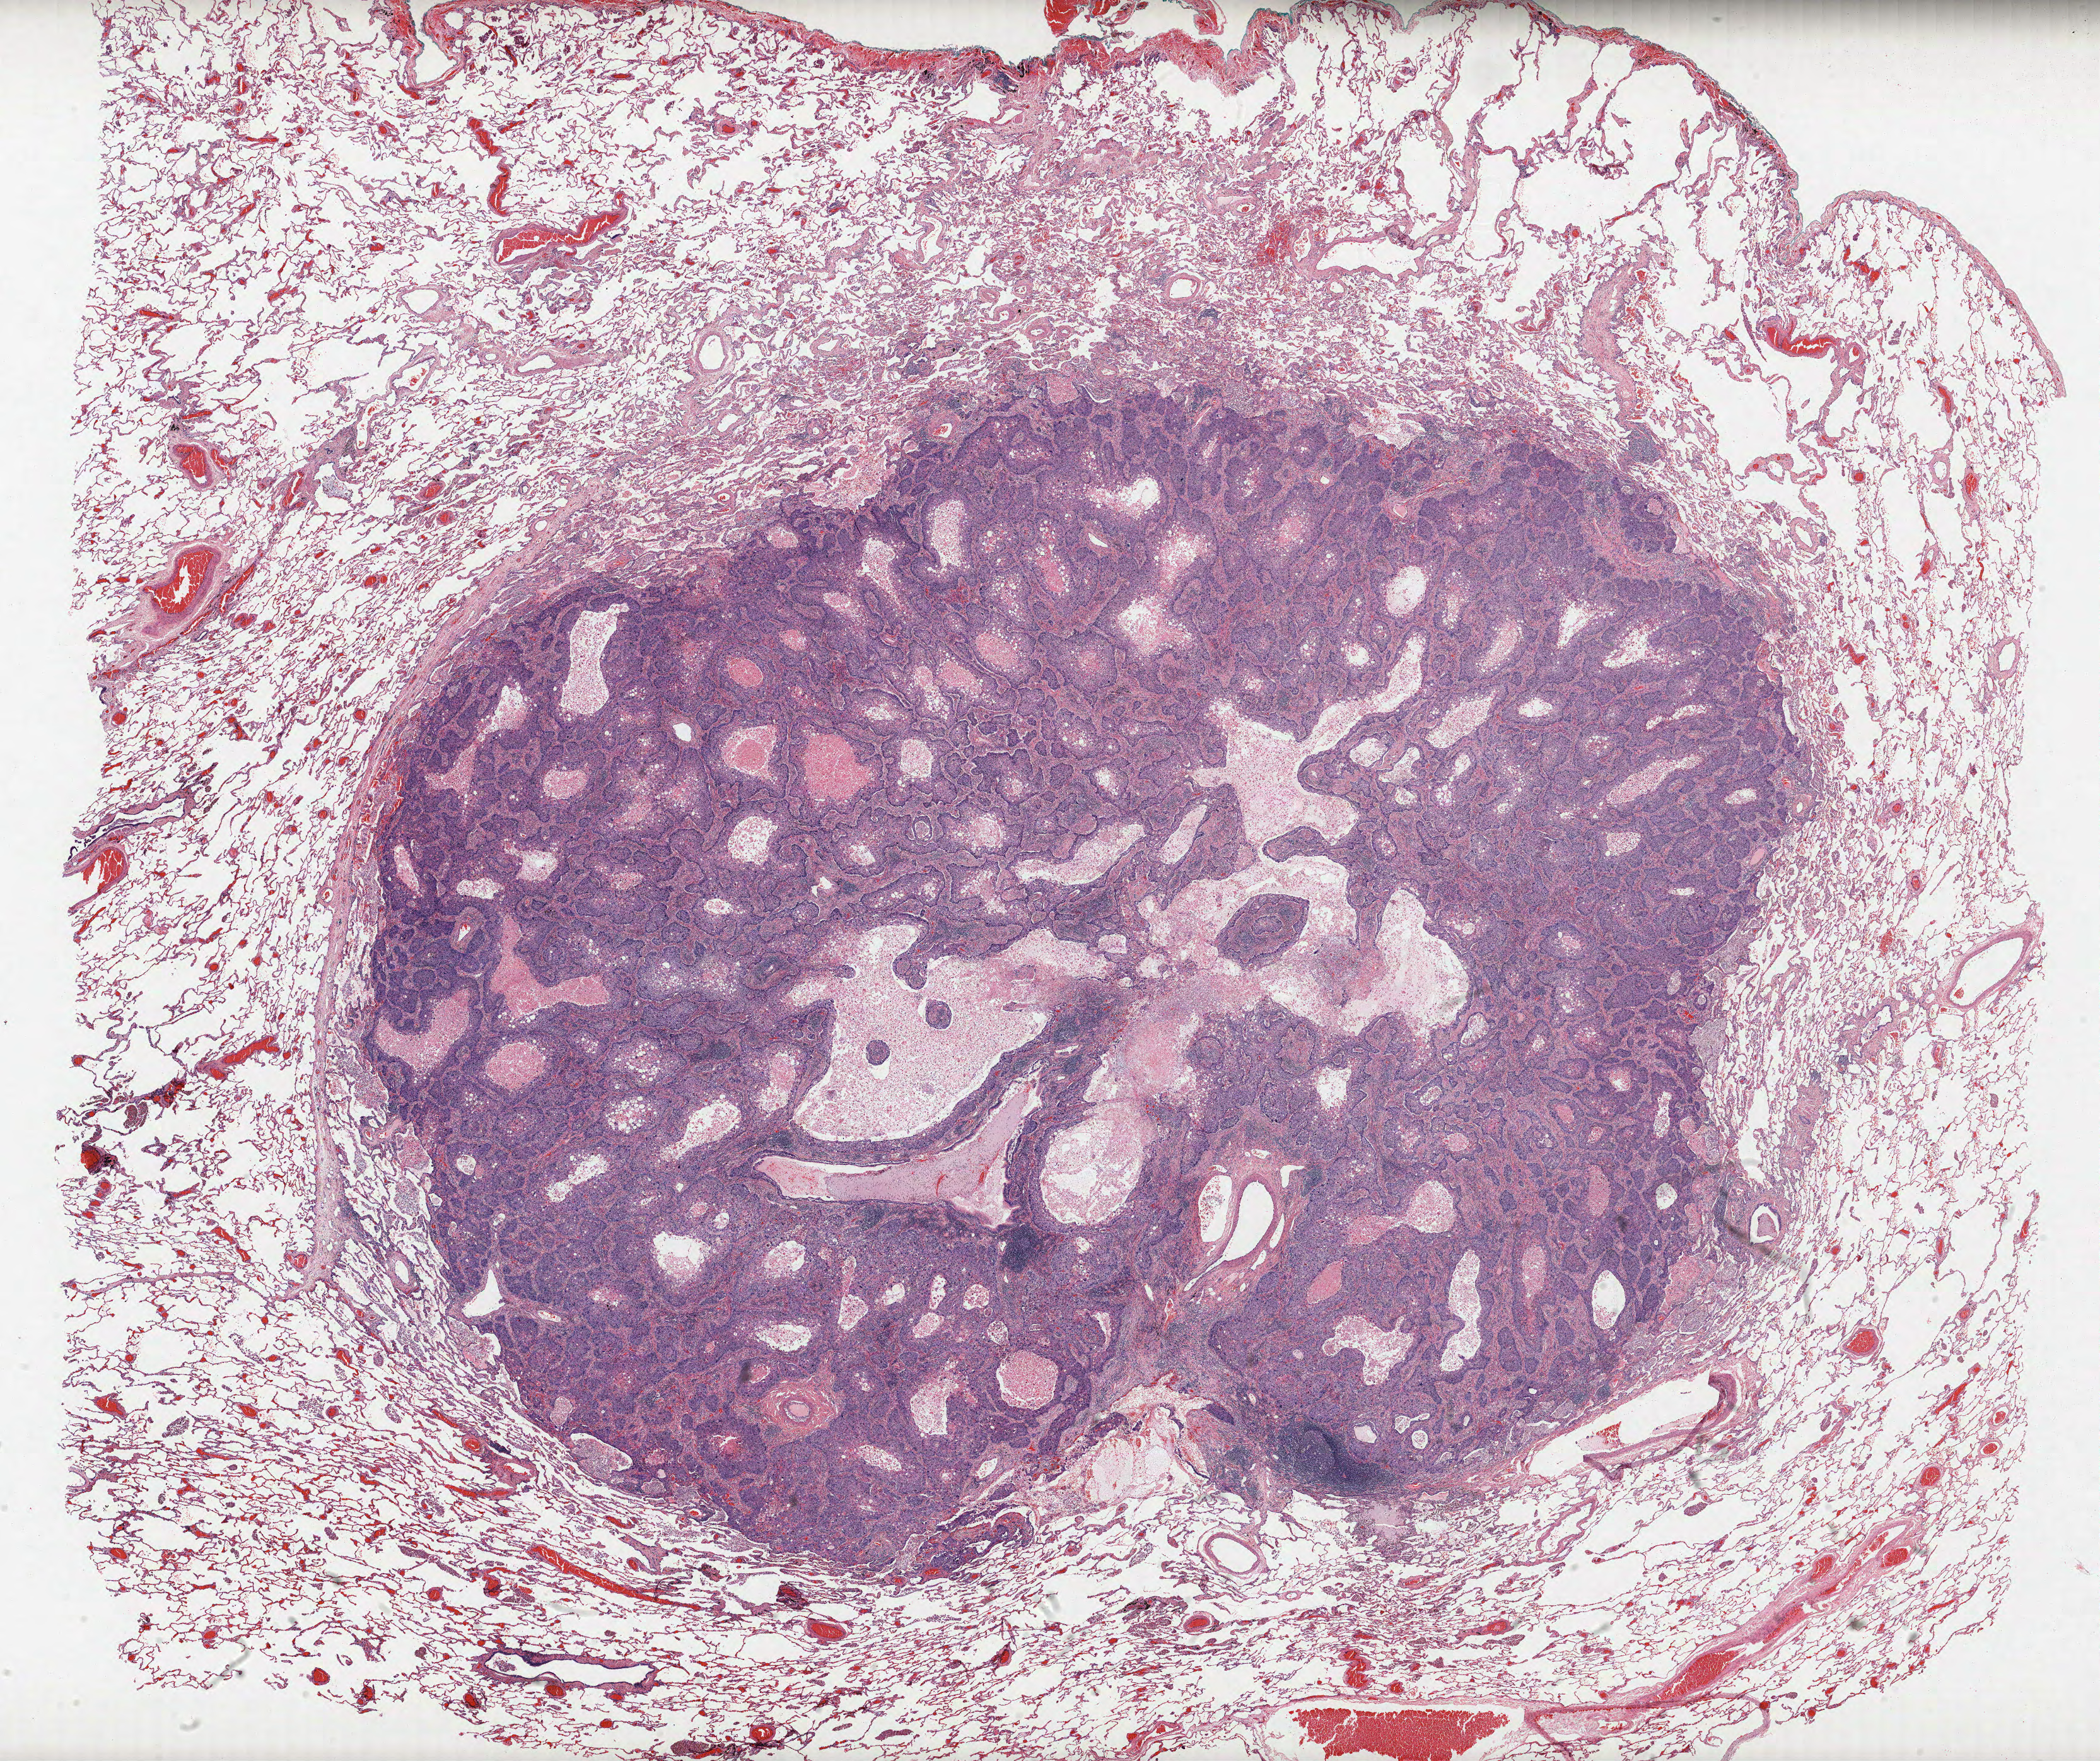
H&E-stained whole-slide image, a low-resolution overview of the entire scanned area, about 26.6 x 22.3 mm (acquisition: 40x scan), FFPE section, lung. Male patient, aged 65 at enrolment. Current smoker at enrolment. Grade: moderately differentiated (G2).
- primary tumour location (clinical record): left upper lobe
- participant's lung-cancer diagnosis: Squamous cell carcinoma, NOS
- tumour size (pathology): 25 mm
- stage (AJCC 6th edition): IA